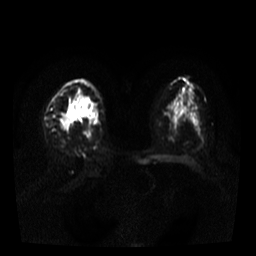
Breast MRI, one axial slice; diffusion-weighted series; image 2 of 4 stored at this slice position (different b-values; order by instance number); 3 T; 5 mm slice thickness; 256 × 256 image matrix, field of view 320 × 320 mm. Female patient.
Structures marked on this image (expert manual segmentation):
- tumour on diffusion-weighted imaging: bounding box (x1, y1, x2, y2) in pixels: (57, 106, 73, 129)